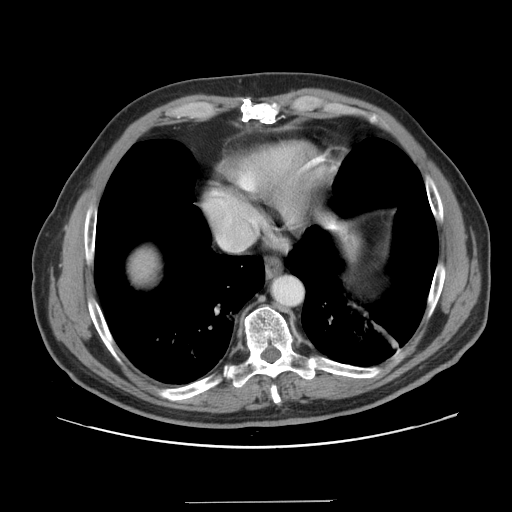
Contrast-enhanced abdominal CT, one axial slice. Slice 146 of 151 in the series (ordered by position). Intravenous contrast given. Soft-tissue window (W 400 / L 40 HU). 2.5 mm slice thickness. 512 × 512 image matrix, field of view 399 × 399 mm. Male patient, age 63 years. From the clinical record (not read from this slice): diagnosis: colorectal cancer liver metastases, imaged before liver resection; multiple liver metastases: no; largest metastasis: 2.1 cm; chemotherapy before resection: no.
Structures marked on this image (expert manual segmentation):
- liver: bounding box <128,245,161,286> (left, top, right, bottom; pixels)
- planned liver remnant (the part of the liver to remain after resection): <128,243,161,286>